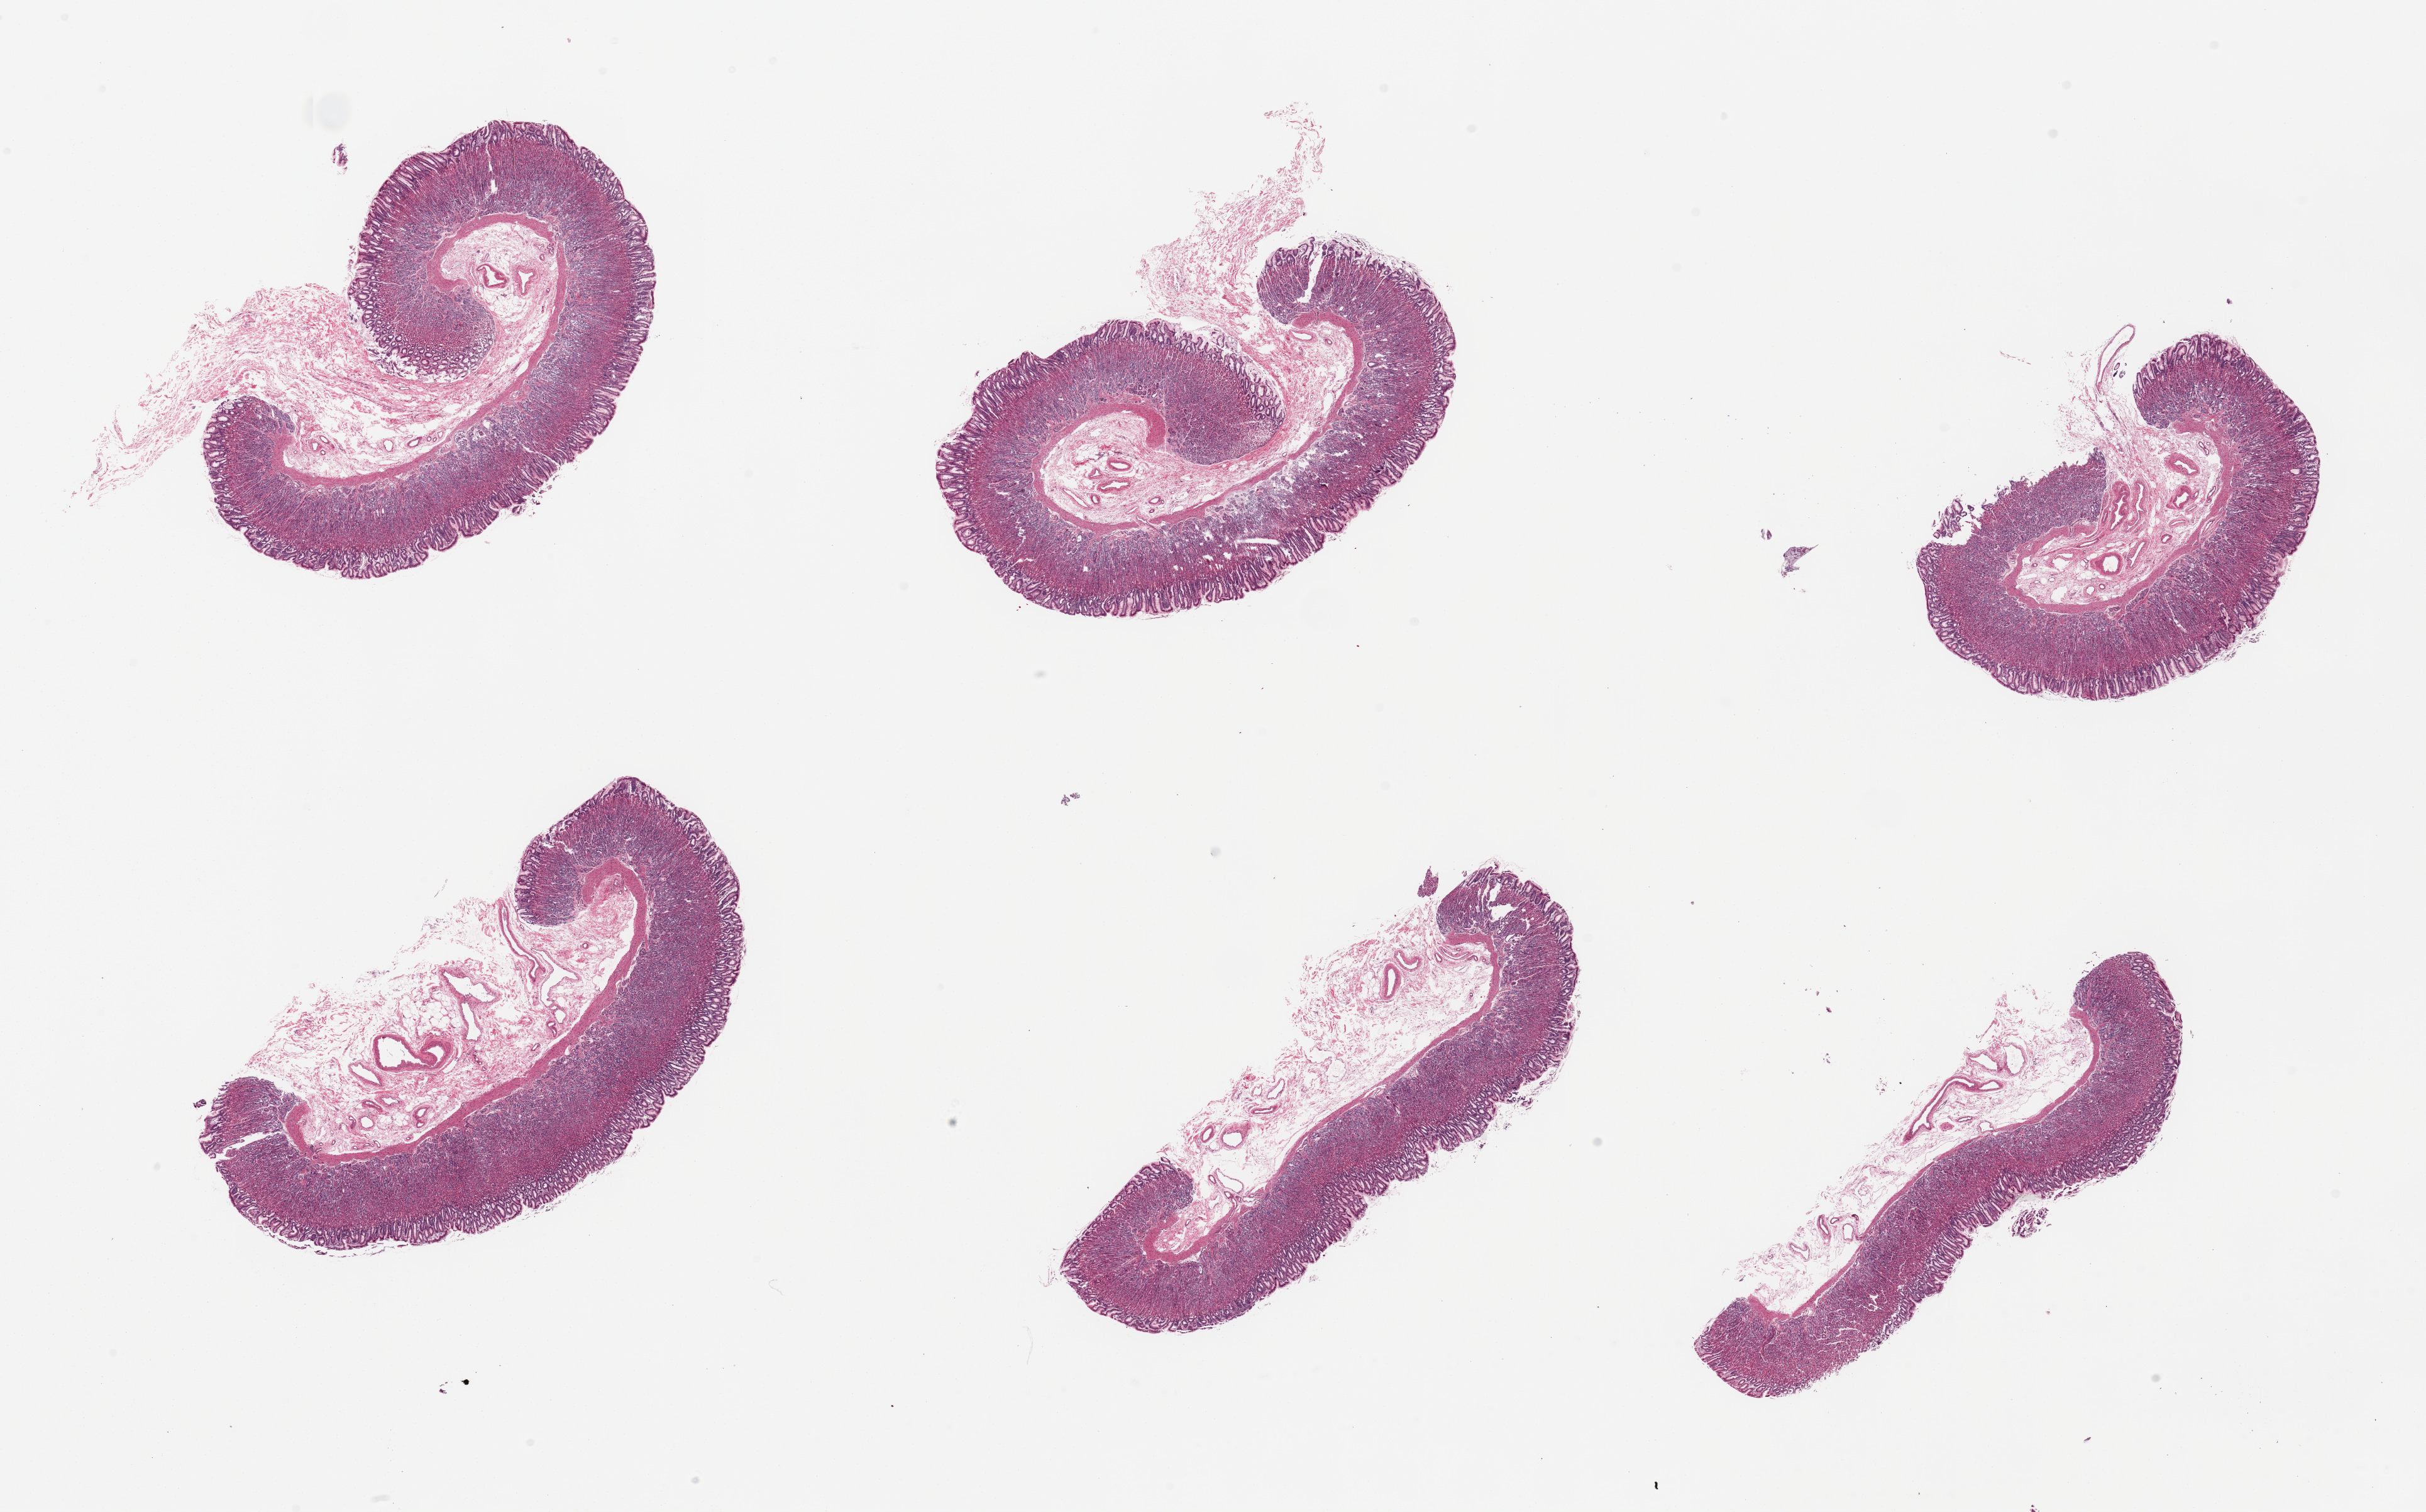
Whole-slide image, H&E stain, brightfield — shown as a low-resolution overview of the whole scanned area (about 30.5 x 19.0 mm, from a 20x scan). PAXgene-fixed paraffin-embedded (PFPE) section. Target tissue: stomach. Tissue donor sample. Donor sex: male.
* review note (as recorded): 6 pieces; mucosa and submucosa, well preserved